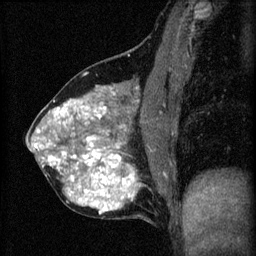
Breast MRI (dynamic contrast-enhanced), one sagittal slice; position 28 of 60 along the scan axis; 3 images stored at this slice position (order not interpretable as contrast timing); 1.5 T; TE 4.2 ms, TR 8.2 ms; 256 × 256 image matrix. Female patient, age 40 years.
Outlined on this slice (semi-automatic segmentation, software-assisted and operator-edited):
- analysis volume of interest (the breast-tissue region the enhancement analysis was run in; not a lesion): bounding box [x1, y1, x2, y2] px = [26, 76, 179, 219]
- tumour enhancement mask (voxels above the 70 % enhancement threshold inside the analysis volume of interest): [34, 94, 141, 215]